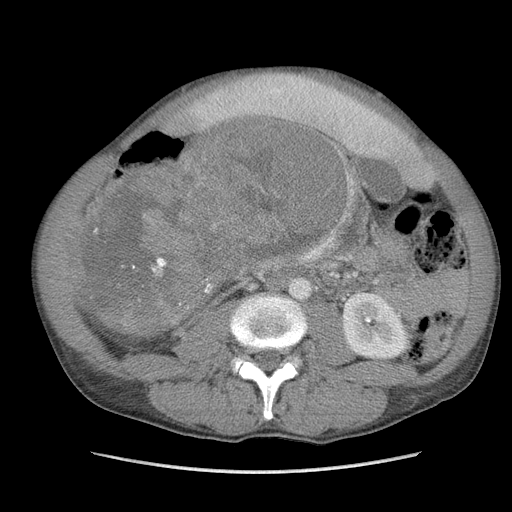
Contrast-enhanced abdominal CT, one axial slice; slice 47 of 115 in the series (ordered by position); soft-tissue window (W 400 / L 40 HU); 5 mm slice thickness; 512 × 512 image matrix, field of view 360 × 360 mm. Male patient. From the clinical record (not read from this slice): diagnosis: adrenocortical carcinoma; tumour side: right adrenal; Ki-67 index: 13 %; stage (as recorded): 3.
Annotated regions visible in this slice (semi-automatic segmentation, software-assisted and operator-edited):
- mass: bounding box (x1, y1, x2, y2) in pixels: (84, 121, 339, 329)